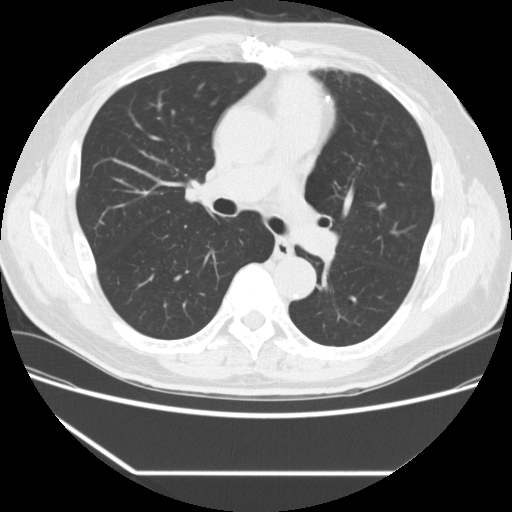
Chest CT (low-dose screening protocol), one axial image; baseline annual screen; lung window (W 1500 / L -600 HU); 2.5 mm slice thickness; slice 97 of 247 in the series; 512 × 512 image matrix, field of view 370 × 370 mm. Male participant, aged 66 years at enrolment. Former smoker at enrolment.
Expert reader's lesion annotation, bounding box <325,172,356,200> (left, top, right, bottom; pixels). Screening reader's record for this exam (one nodule recorded; not confirmed to be the boxed lesion): non-calcified nodule or mass ≥4 mm, right lower lobe, 4 × 4 mm, smooth margins, soft tissue attenuation. Note: the box lies in the patient's left hemithorax on this image, whereas the reader's record names the right lung; they may be different findings. Lung cancer was diagnosed 792 days after this screen: squamous cell carcinoma, NOS, left upper lobe, poorly differentiated (G3), stage IA (AJCC 6th edition), 27 mm at pathology.